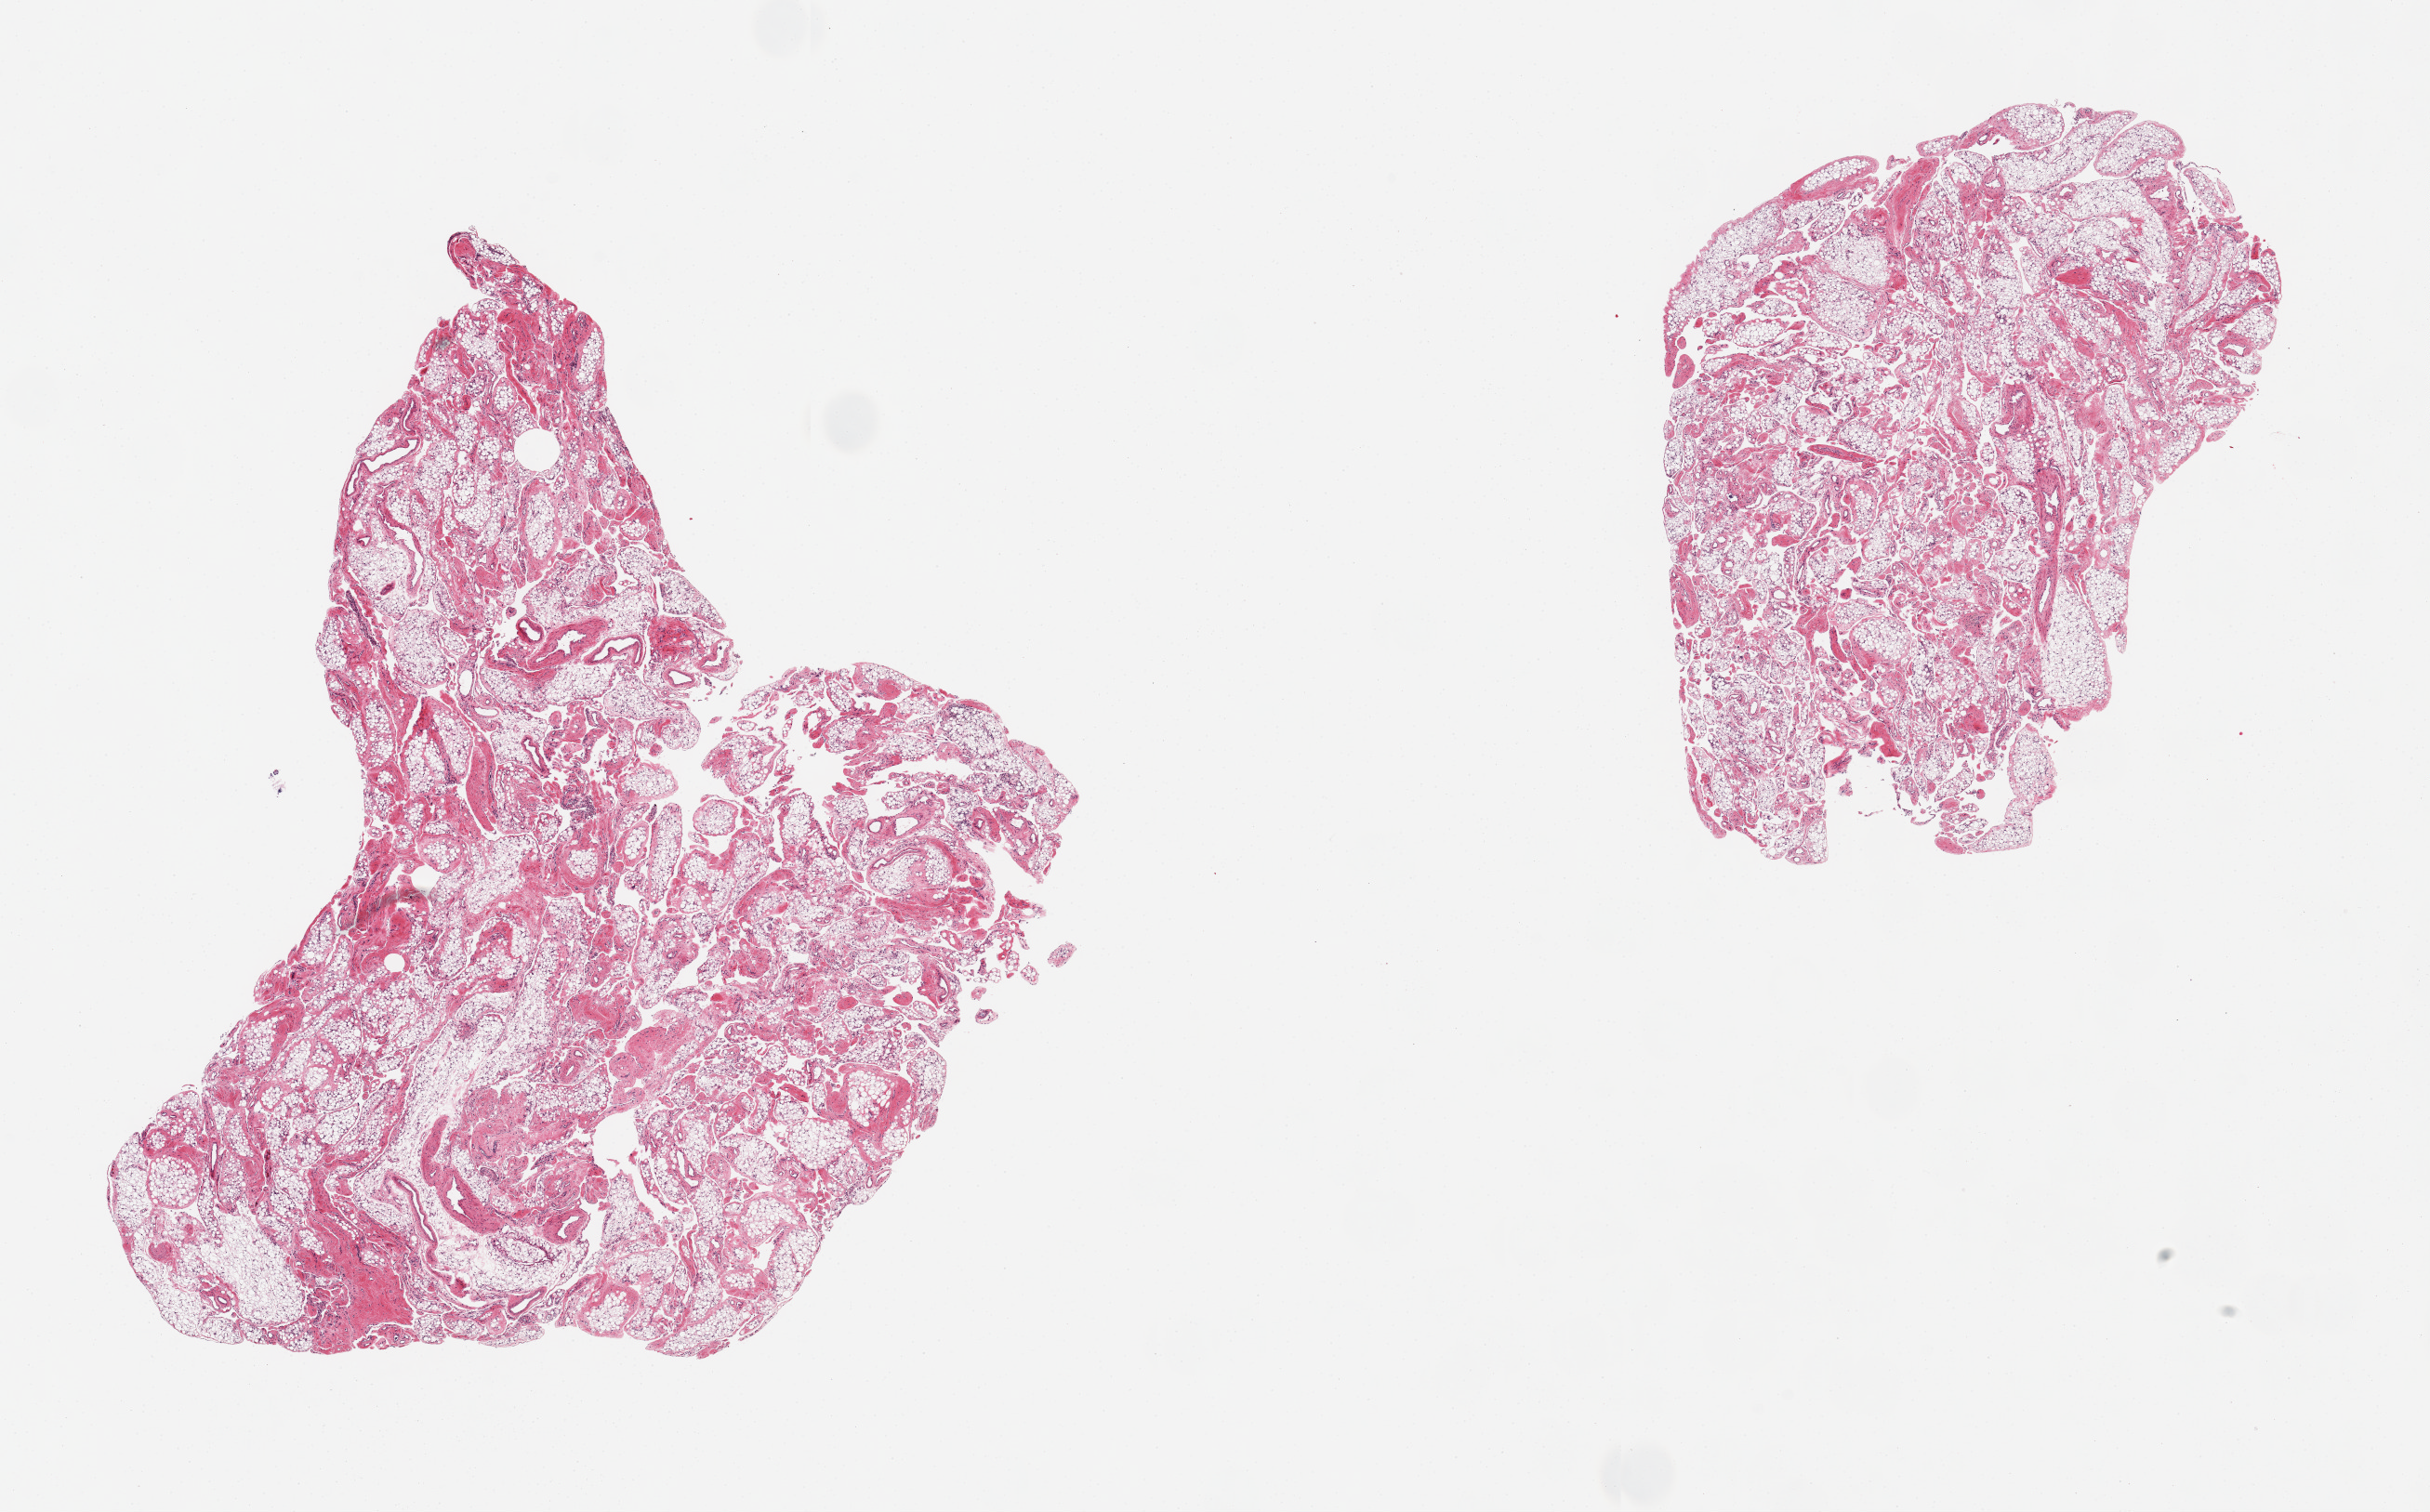
Whole-slide image, H&E stain, whole scanned area (about 20.7 x 12.9 mm, slide scanned at 20x) shown as a low-resolution overview, PAXgene-fixed paraffin-embedded (PFPE) section, section of omentum (target tissue), donor tissue sample. Donor: female.
Reviewer comment on this tissue sample: 2 pieces, marked reactive mesothelial hyperplasia/fibrosis.